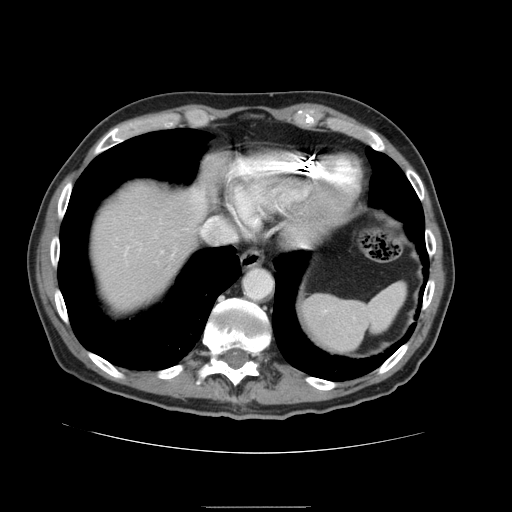
Contrast-enhanced abdominal CT, one axial slice. Slice 133 of 168 in the series (ordered by position). 120 kVp. Intravenous contrast given. Soft-tissue window (W 400 / L 40 HU). 2.5 mm slice thickness. 512 × 512 image matrix, field of view 386 × 386 mm. Male patient, age 74 years. From the clinical record (not read from this slice): diagnosis: colorectal cancer liver metastases, imaged before liver resection; multiple liver metastases: no; largest metastasis: 14.5 cm; chemotherapy before resection: no.
Outlined on this slice (expert manual segmentation):
- liver: bounding box (x1, y1, x2, y2) in pixels: (89, 180, 210, 316)
- planned liver remnant (the part of the liver to remain after resection): (89, 179, 209, 320)